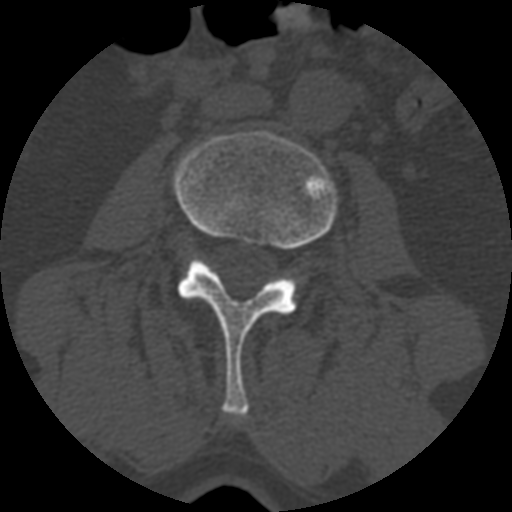
CT including the spine, one axial slice; slice 304 of 399 in the series (ordered by position); 120 kVp; bone window (W 1800 / L 400 HU); 1.25 mm slice thickness; 512 × 512 image matrix. Patient age 71 years. Case-level facts recorded for this patient, not image findings: primary cancer: prostate.
Outlined on this slice (semi-automatically segmented with operator editing):
- L3 vertebra: box from (x=172, y=129) to (x=340, y=418) px